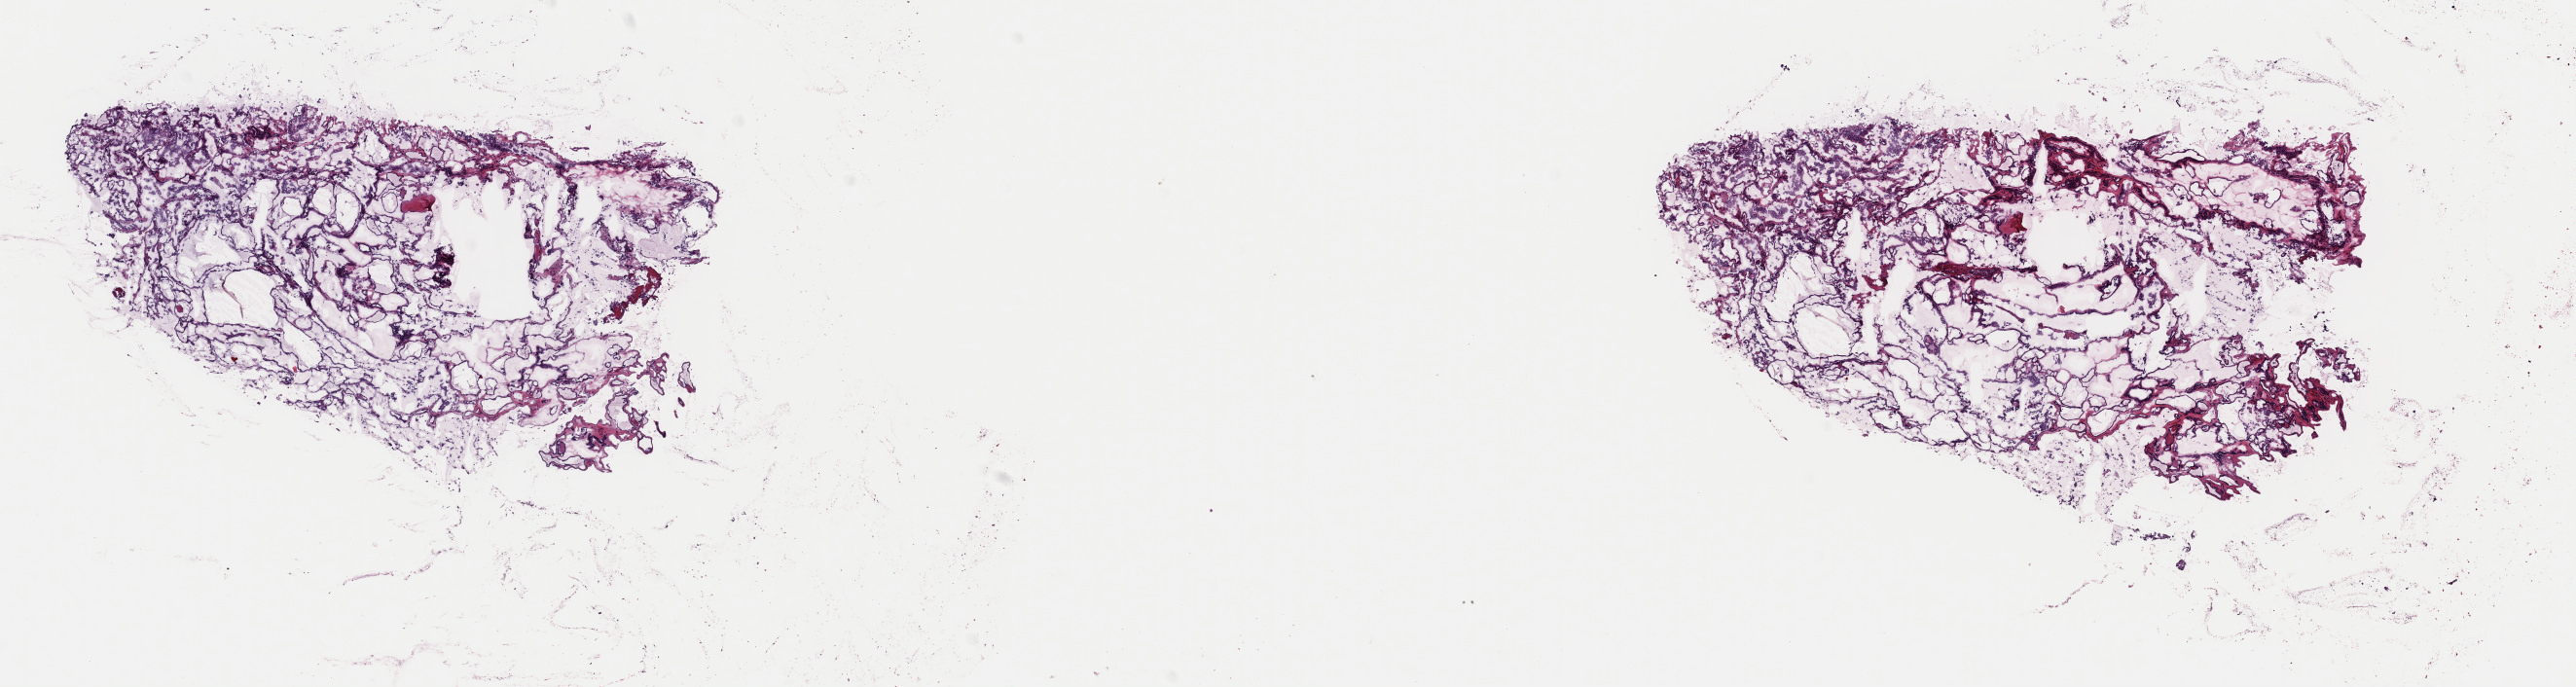
Digitized H&E-stained tissue section (whole slide) — low-resolution overview of the scanned area, about 20.9 x 5.6 mm. Frozen section from the top of the tissue portion. Thyroid, primary tumour sample. Female, age 42 years at initial diagnosis. Pathologist review of this section (percent, as recorded): tumour cells 90%, tumour nuclei 100%, normal cells 0%, stromal cells 10%, necrosis 0%. Inflammatory infiltration, as recorded: lymphocyte infiltration 1%, monocyte infiltration 3%, neutrophil infiltration 0%.
Pathologic diagnosis: Papillary adenocarcinoma, NOS (thyroid gland). AJCC pathologic stage: I (6th edition). Lymph nodes positive (case pathology): 4 of 8 examined.